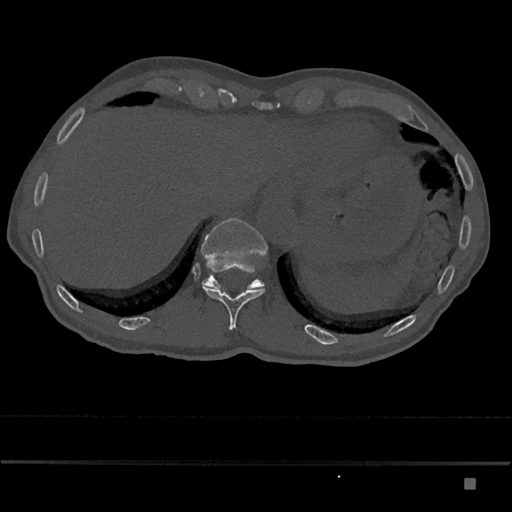
CT including the spine, one axial slice; position 654 of 797 along the scan axis; reconstruction kernel Br40s/3; 120 kVp; bone window (W 1800 / L 400 HU); 0.5 mm slice thickness; 512 × 512 image matrix. Male patient, age 72 years. From the clinical record (not read from this slice): primary cancer: prostate.
Structures marked on this image (semi-automatic segmentation, software-assisted and operator-edited):
- T11 vertebra: bounding box (x1, y1, x2, y2) in pixels: (202, 283, 265, 330)
- T12 vertebra: (201, 218, 268, 290)